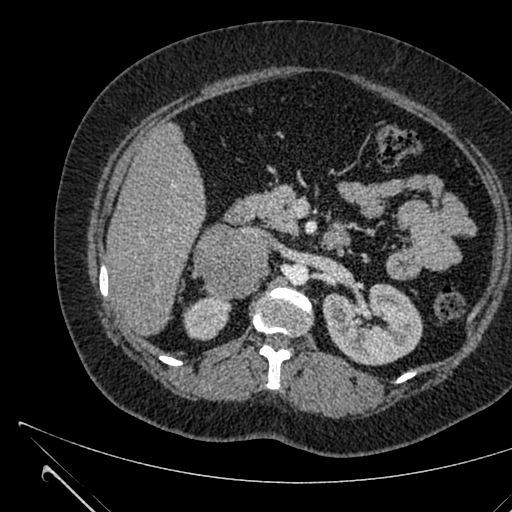
Contrast-enhanced abdominal CT, one axial slice. Slice 378 of 731 in the series (ordered by position). 120 kVp. Intravenous contrast given. Soft-tissue window (W 400 / L 40 HU). 1 mm slice thickness. 512 × 512 image matrix, field of view 376 × 376 mm. Patient: female, 36 years. From the clinical record (not read from this slice): diagnosis: adrenocortical carcinoma; tumour side: right adrenal; tumour size at pathology: 10 cm; Ki-67 index: 20 %; stage (as recorded): 4.
Structures marked on this image (semi-automatically segmented with operator editing):
- mass: bounding box (x1, y1, x2, y2) in pixels: (197, 224, 269, 299)